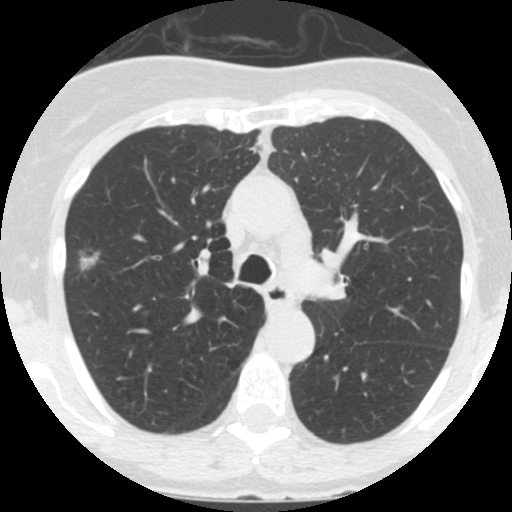
Chest CT (low-dose screening protocol), one axial image, third annual screen, lung window (W 1500 / L -600 HU), 2.5 mm slice thickness, standard (soft-tissue) reconstruction kernel (STANDARD), 120 kVp. Female participant, aged 60 years at enrolment. Current smoker at enrolment.
Expert-annotated lung lesion, bounding box <61,232,110,284> (left, top, right, bottom; pixels). The exam's reader record, not a measurement of the box and not confirmed to be the same lesion: non-calcified nodule or mass ≥4 mm, right upper lobe, 12 × 12 mm, smooth margins, ground glass attenuation, pre-existing on the prior screen: yes; interval growth: yes. Official screen result: positive, other. Lung cancer was diagnosed 56 days after this screen: bronchiolo-alveolar adenocarcinoma, NOS, right upper lobe, well differentiated (G1), stage IA (AJCC 6th edition), 11 mm at pathology.